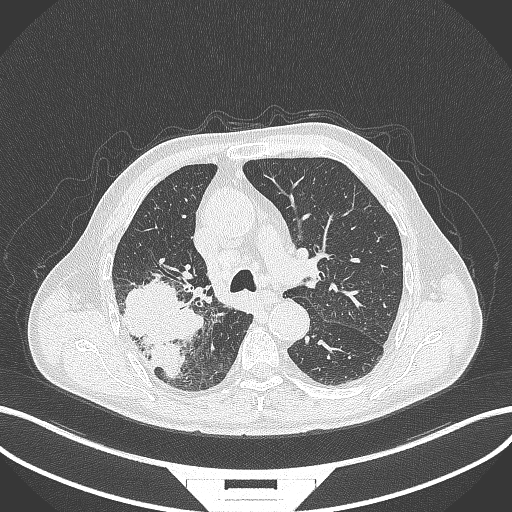
Chest CT, one axial slice. Slice 273 of 429 in the series (ordered by position). Reconstruction kernel B70f. Lung window (W 1500 / L -600 HU). 512 × 512 image matrix, field of view 400 × 400 mm. Patient: male, 72 years. Case-level facts recorded for this patient, not image findings: clinical TNM (as recorded): T3 N2 M0.
Structures marked on this image (bounding box drawn by a radiologist):
- lung tumour (recorded histology: adenocarcinoma): box from (x=120, y=274) to (x=209, y=380) px